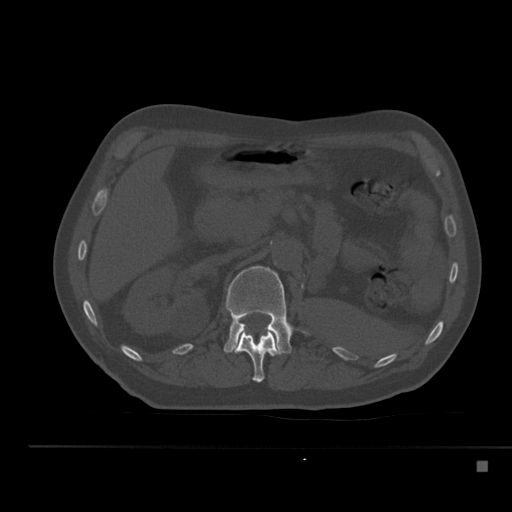
CT including the spine, one axial slice; slice 216 of 517 in the series (ordered by position); reconstruction kernel Br40s; 120 kVp; bone window (W 1800 / L 400 HU); 1.5 mm slice thickness; 512 × 512 image matrix. Male patient, age 70 years. From the clinical record (not read from this slice): primary cancer: renal; vertebrae with lytic lesions (as recorded): T4, T6, T10, T12, L3, L4, L5.
Annotated regions visible in this slice (semi-automatic segmentation, software-assisted and operator-edited):
- L1 vertebra: bounding box [x1, y1, x2, y2] px = [224, 265, 293, 355]
- T12 vertebra: [233, 329, 279, 383]